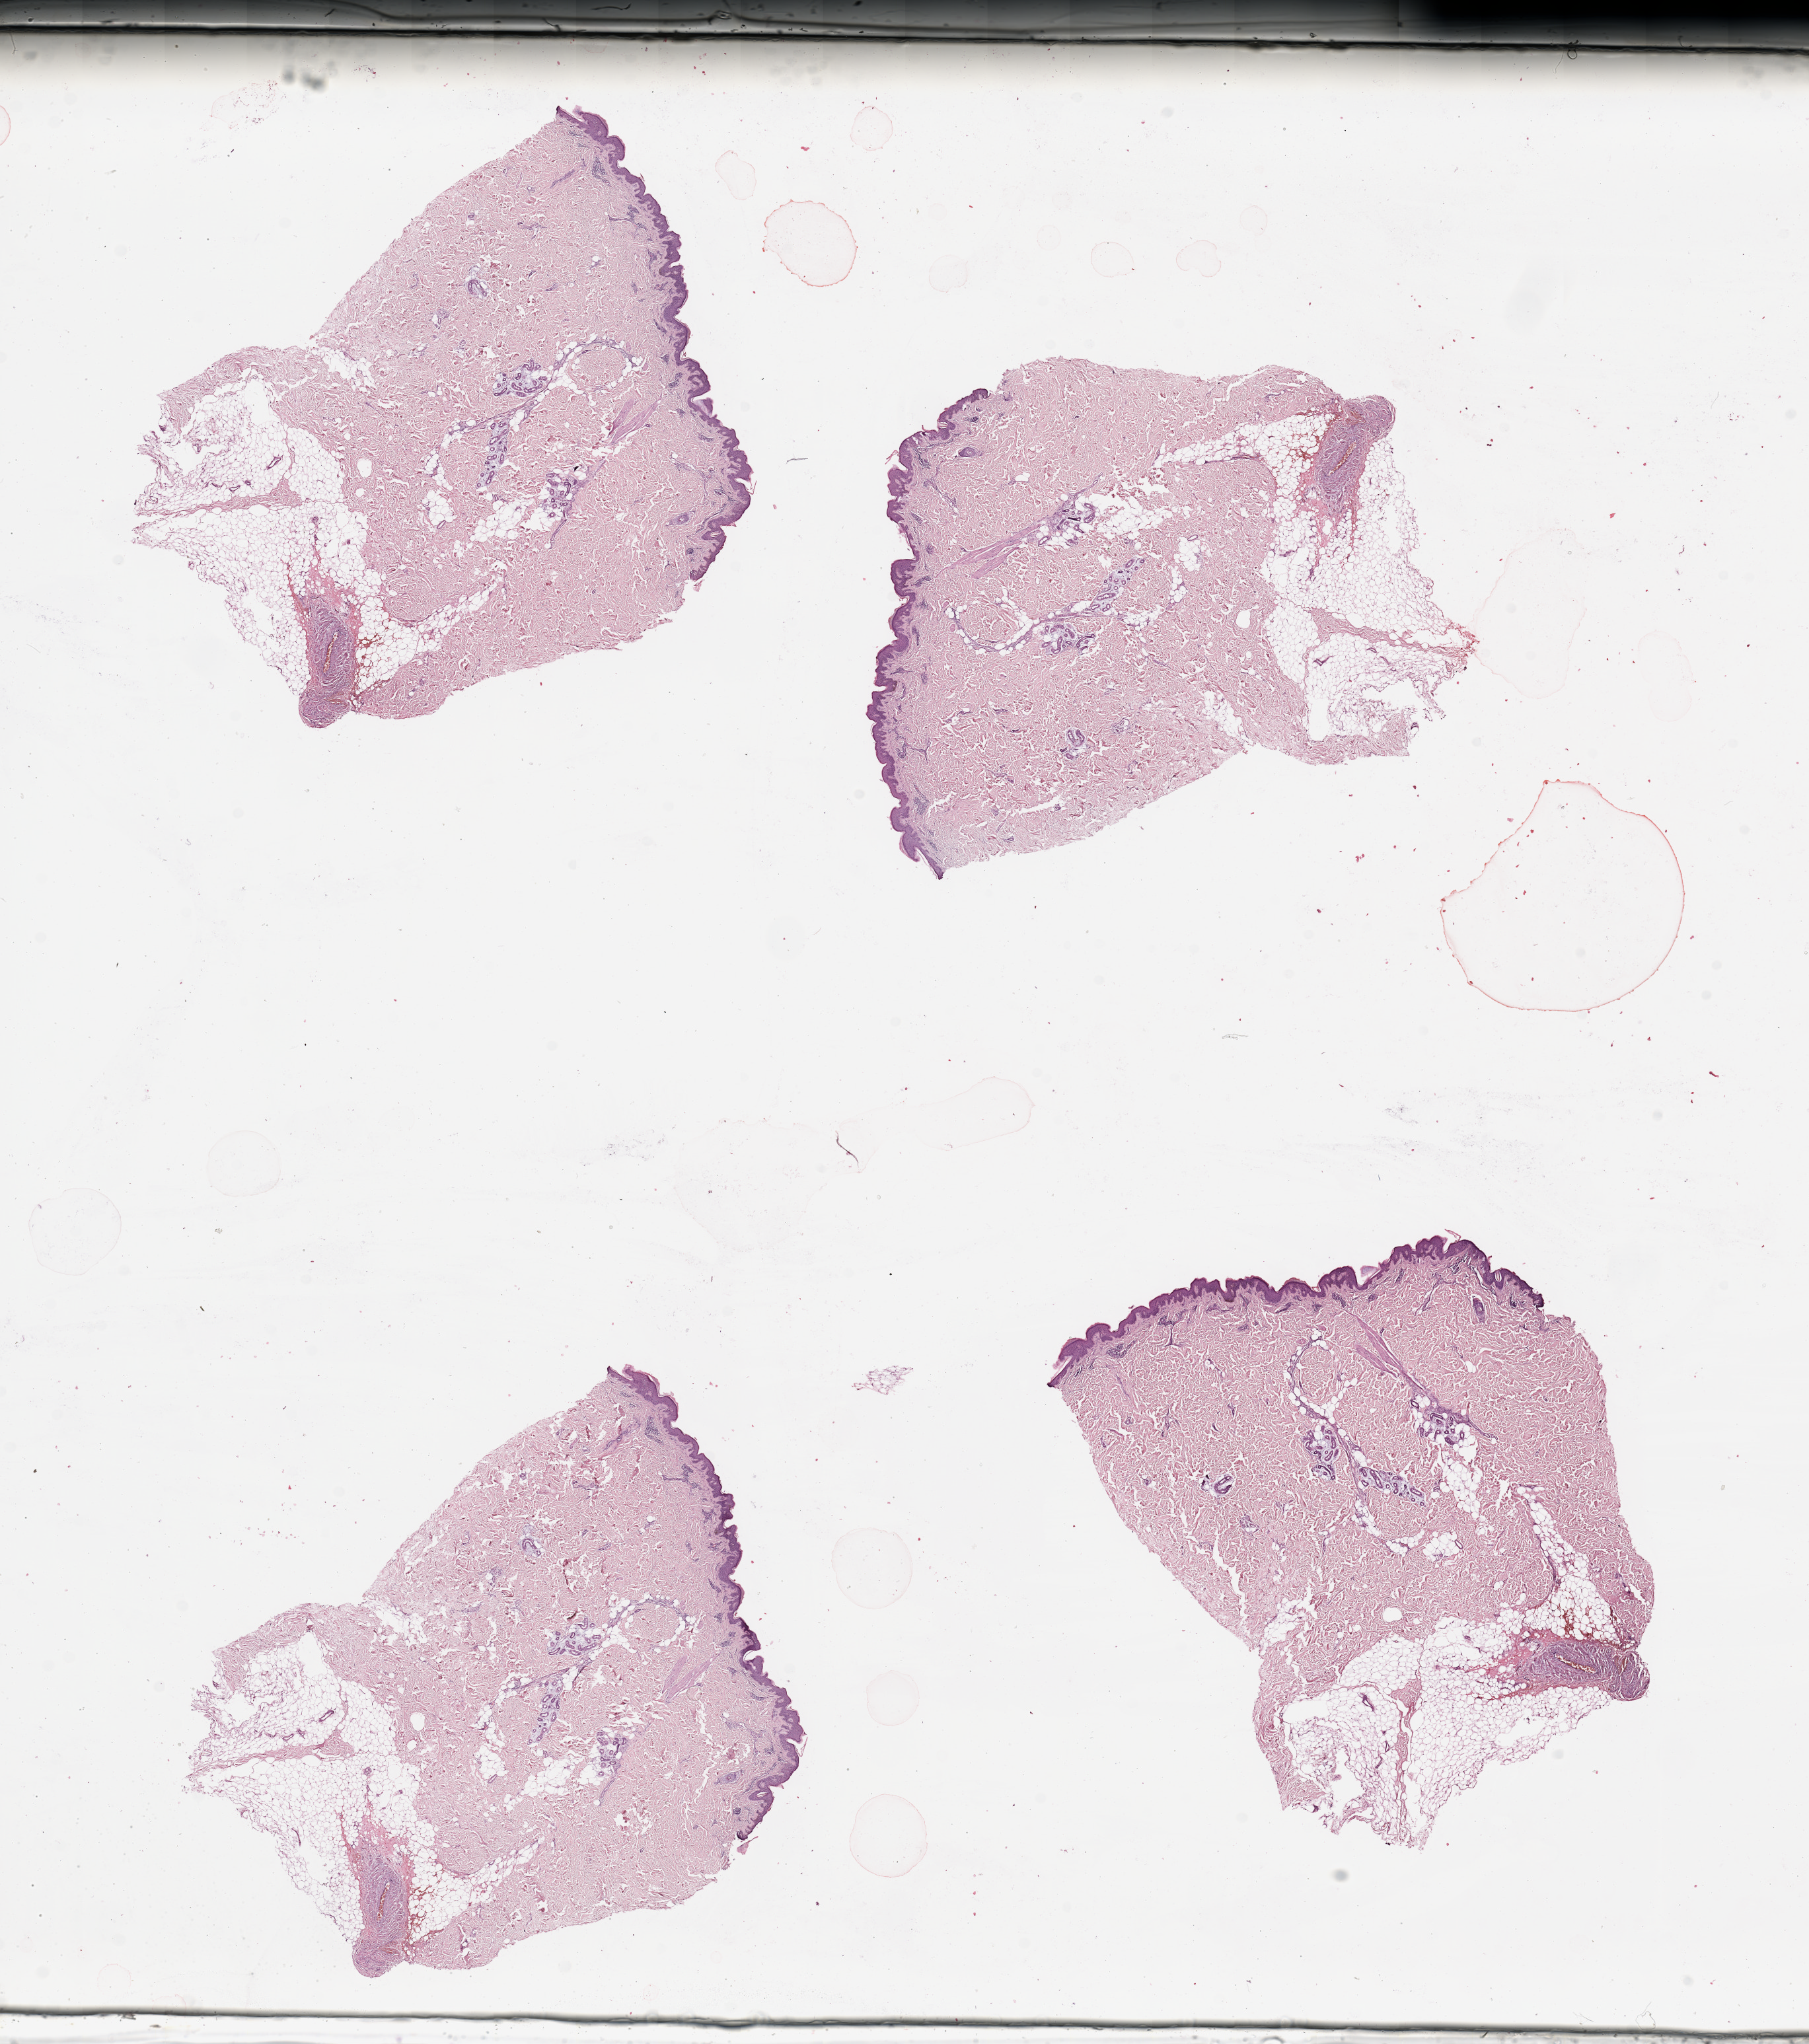
H&E whole-slide image, low-resolution overview of the scanned area, about 21.7 x 24.5 mm (acquisition: 20x scan), normal (non-tumour) tissue (melanoma cohort); sampled site not recorded. 60-year-old male patient.
This section: normal (non-tumour) tissue from the same patient. Patient diagnosis: Malignant melanoma, NOS.